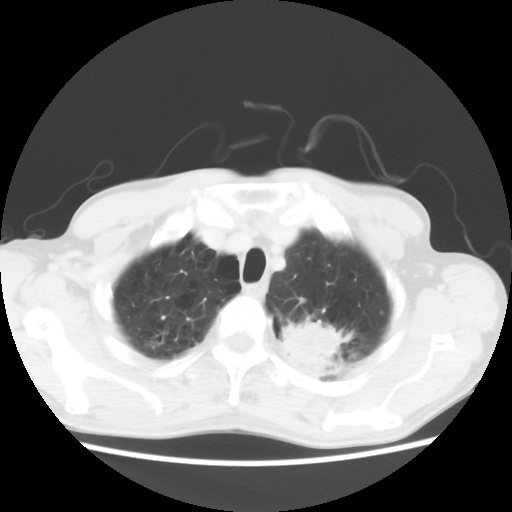
Chest CT, one axial slice; lung window (W 1500 / L -600 HU); 5 mm slice thickness; 512 × 512 image matrix, field of view 346 × 346 mm. Patient: male, 63 years. From the clinical record (not read from this slice): clinical TNM (as recorded): T2 N0 M0.
Annotated regions visible in this slice (bounding box drawn by a radiologist):
- lung tumour (recorded histology: adenocarcinoma): bounding box (x1, y1, x2, y2) in pixels: (277, 317, 355, 389)